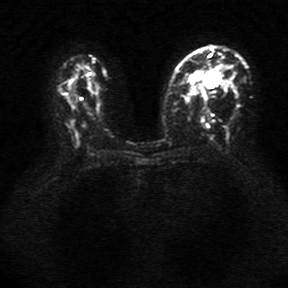
Breast MRI, one axial slice; position 21 of 34 along the scan axis; diffusion-weighted series; image 2 of 4 stored at this slice position (different b-values; order by instance number); 1.5 T; 288 × 288 image matrix, field of view 340 × 340 mm. Female patient.
Outlined on this slice (manually delineated by an expert):
- tumour on diffusion-weighted imaging: bounding box (x1, y1, x2, y2) in pixels: (205, 70, 217, 79)